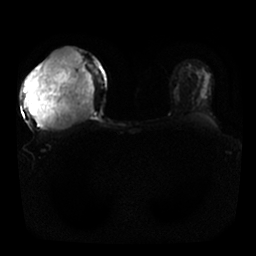
Breast MRI, one axial slice; position 16 of 25 along the scan axis; diffusion-weighted series; image 2 of 4 stored at this slice position (different b-values; order by instance number); 1.5 T; 256 × 256 image matrix, field of view 340 × 340 mm. Female patient.
Outlined on this slice (manually delineated by an expert):
- tumour on diffusion-weighted imaging: bounding box <25,46,96,130> (left, top, right, bottom; pixels)